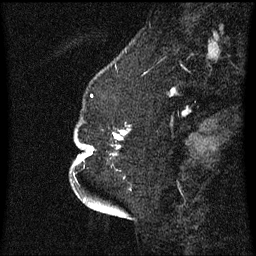
Breast MRI (dynamic contrast-enhanced), one sagittal slice; position 18 of 60 along the scan axis; dynamic contrast-enhanced series, image 2 of 3 at this slice position (ordered by acquisition); 1.5 T; TE 4.2 ms, TR 8.4 ms; 2.3 mm slice thickness; 256 × 256 image matrix, field of view 200 × 200 mm. Patient: female, 52 years. Case-level facts recorded for this patient, not image findings: setting: breast cancer imaged before/during neoadjuvant chemotherapy; receptor status: HR-positive, HER2-negative.
Outlined on this slice (semi-automatically segmented with operator editing):
- analysis volume of interest (the breast-tissue region the enhancement analysis was run in; not a lesion): bounding box [x1, y1, x2, y2] px = [75, 118, 127, 179]
- tumour enhancement mask (voxels above the 70 % enhancement threshold inside the analysis volume of interest): [91, 130, 127, 151]